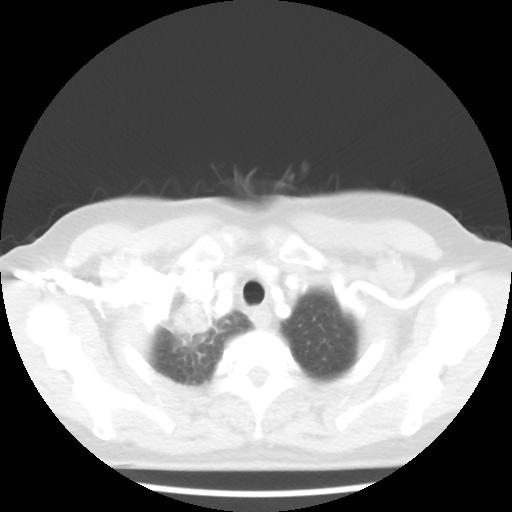
Chest CT, one axial slice; position 40 of 44 along the scan axis; lung window (W 1500 / L -600 HU); 5 mm slice thickness; 512 × 512 image matrix, field of view 316 × 316 mm. Female patient, age 62 years. From the clinical record (not read from this slice): clinical TNM (as recorded): T3 N0 M0; histopathological grade: G3.
Annotated regions visible in this slice (bounding box drawn by a radiologist):
- lung tumour (recorded histology: small cell carcinoma): box from (x=162, y=288) to (x=220, y=347) px